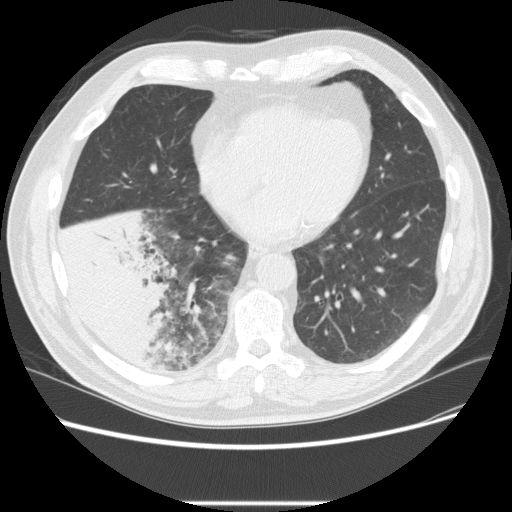
Low-dose screening chest CT, one axial slice. Position 83 of 233 along the scan axis. Reconstruction kernel STANDARD. 120 kVp. Lung window (W 1500 / L -600 HU). 2.5 mm slice thickness. 512 × 512 image matrix.
Outlined on this slice (expert manual segmentation):
- lesion 3 (tumor, lower lobe of right lung): bounding box <56,209,176,366> (left, top, right, bottom; pixels)